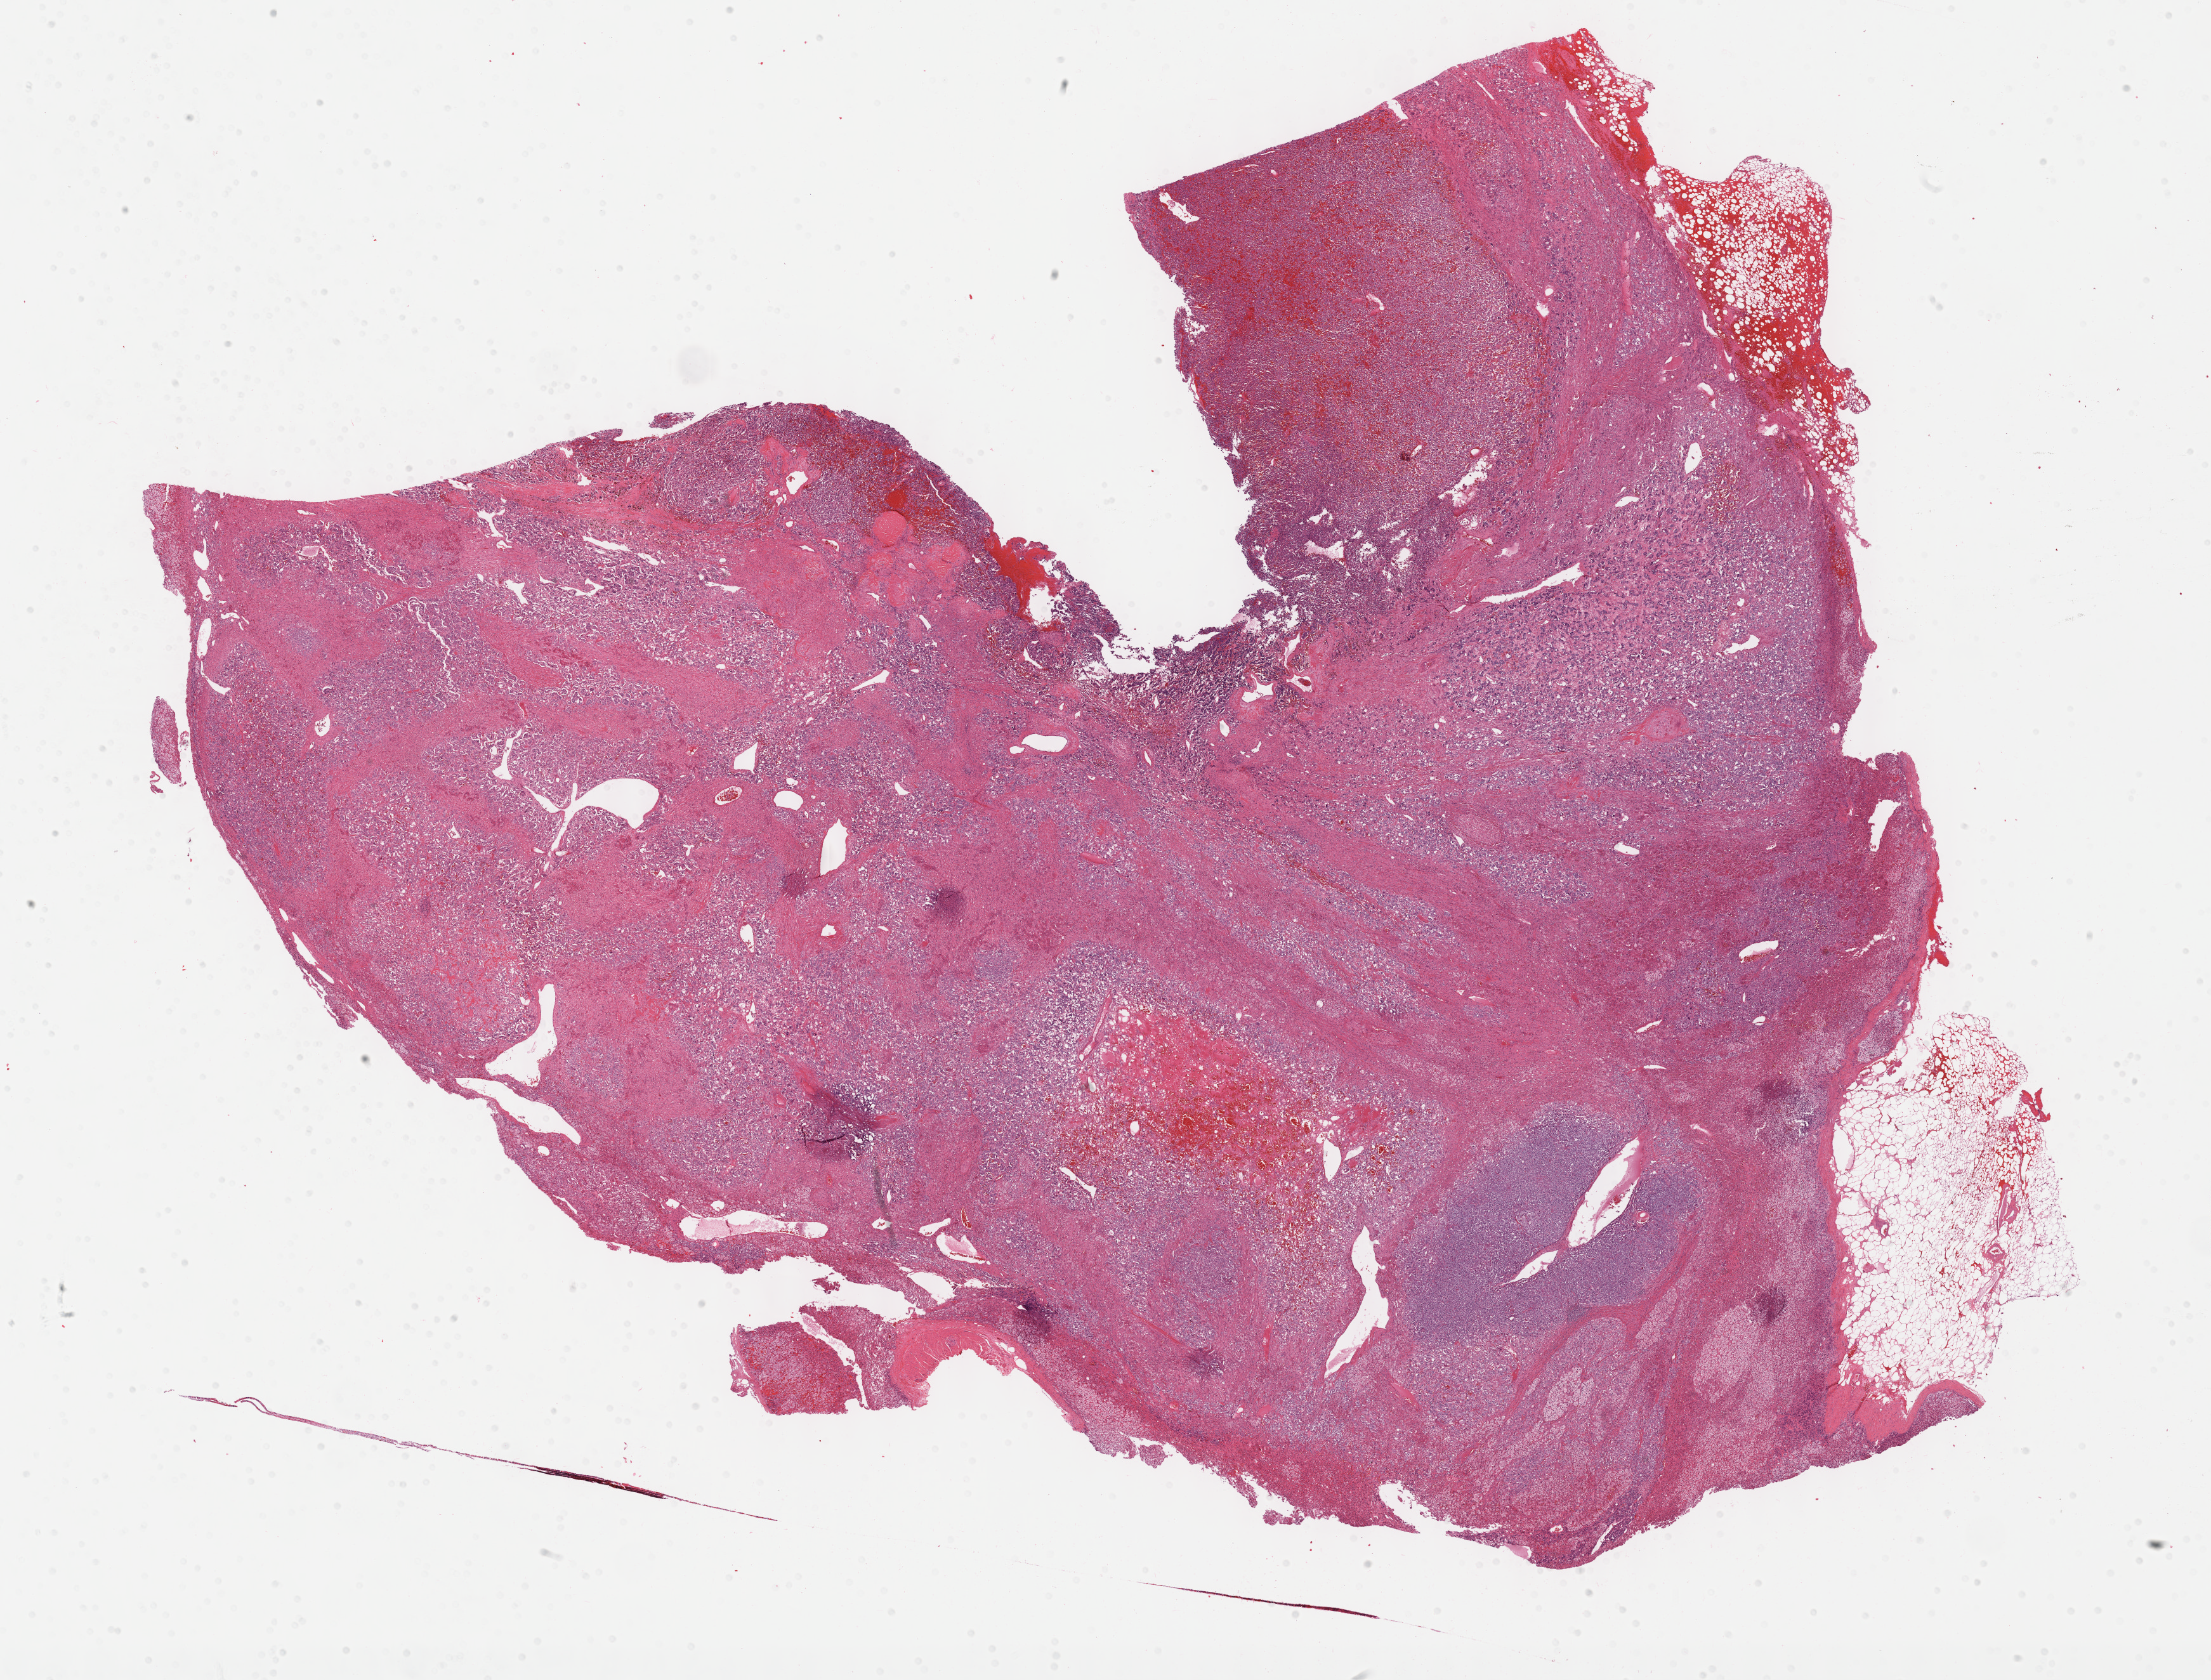
Whole-slide histology image, H&E, low-resolution overview of the scanned area, about 28.2 x 21.4 mm. FFPE section. Sample: primary tumour, adrenal gland. Female, age 44 years at initial diagnosis.
* laterality: right
* pathologic diagnosis: Pheochromocytoma, NOS